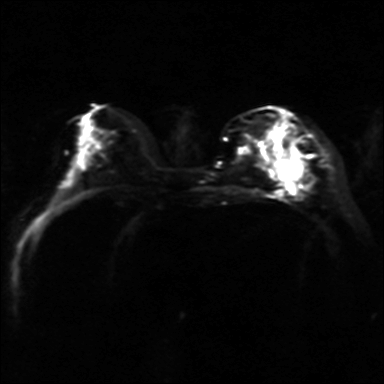
Breast MRI, one axial slice; position 15 of 36 along the scan axis; diffusion-weighted series; image 2 of 4 stored at this slice position (different b-values; order by instance number); 3 T; 384 × 384 image matrix, field of view 320 × 320 mm. Female patient.
Annotated regions visible in this slice (outlined manually by an expert reader):
- tumour on diffusion-weighted imaging: box from (x=276, y=158) to (x=299, y=181) px